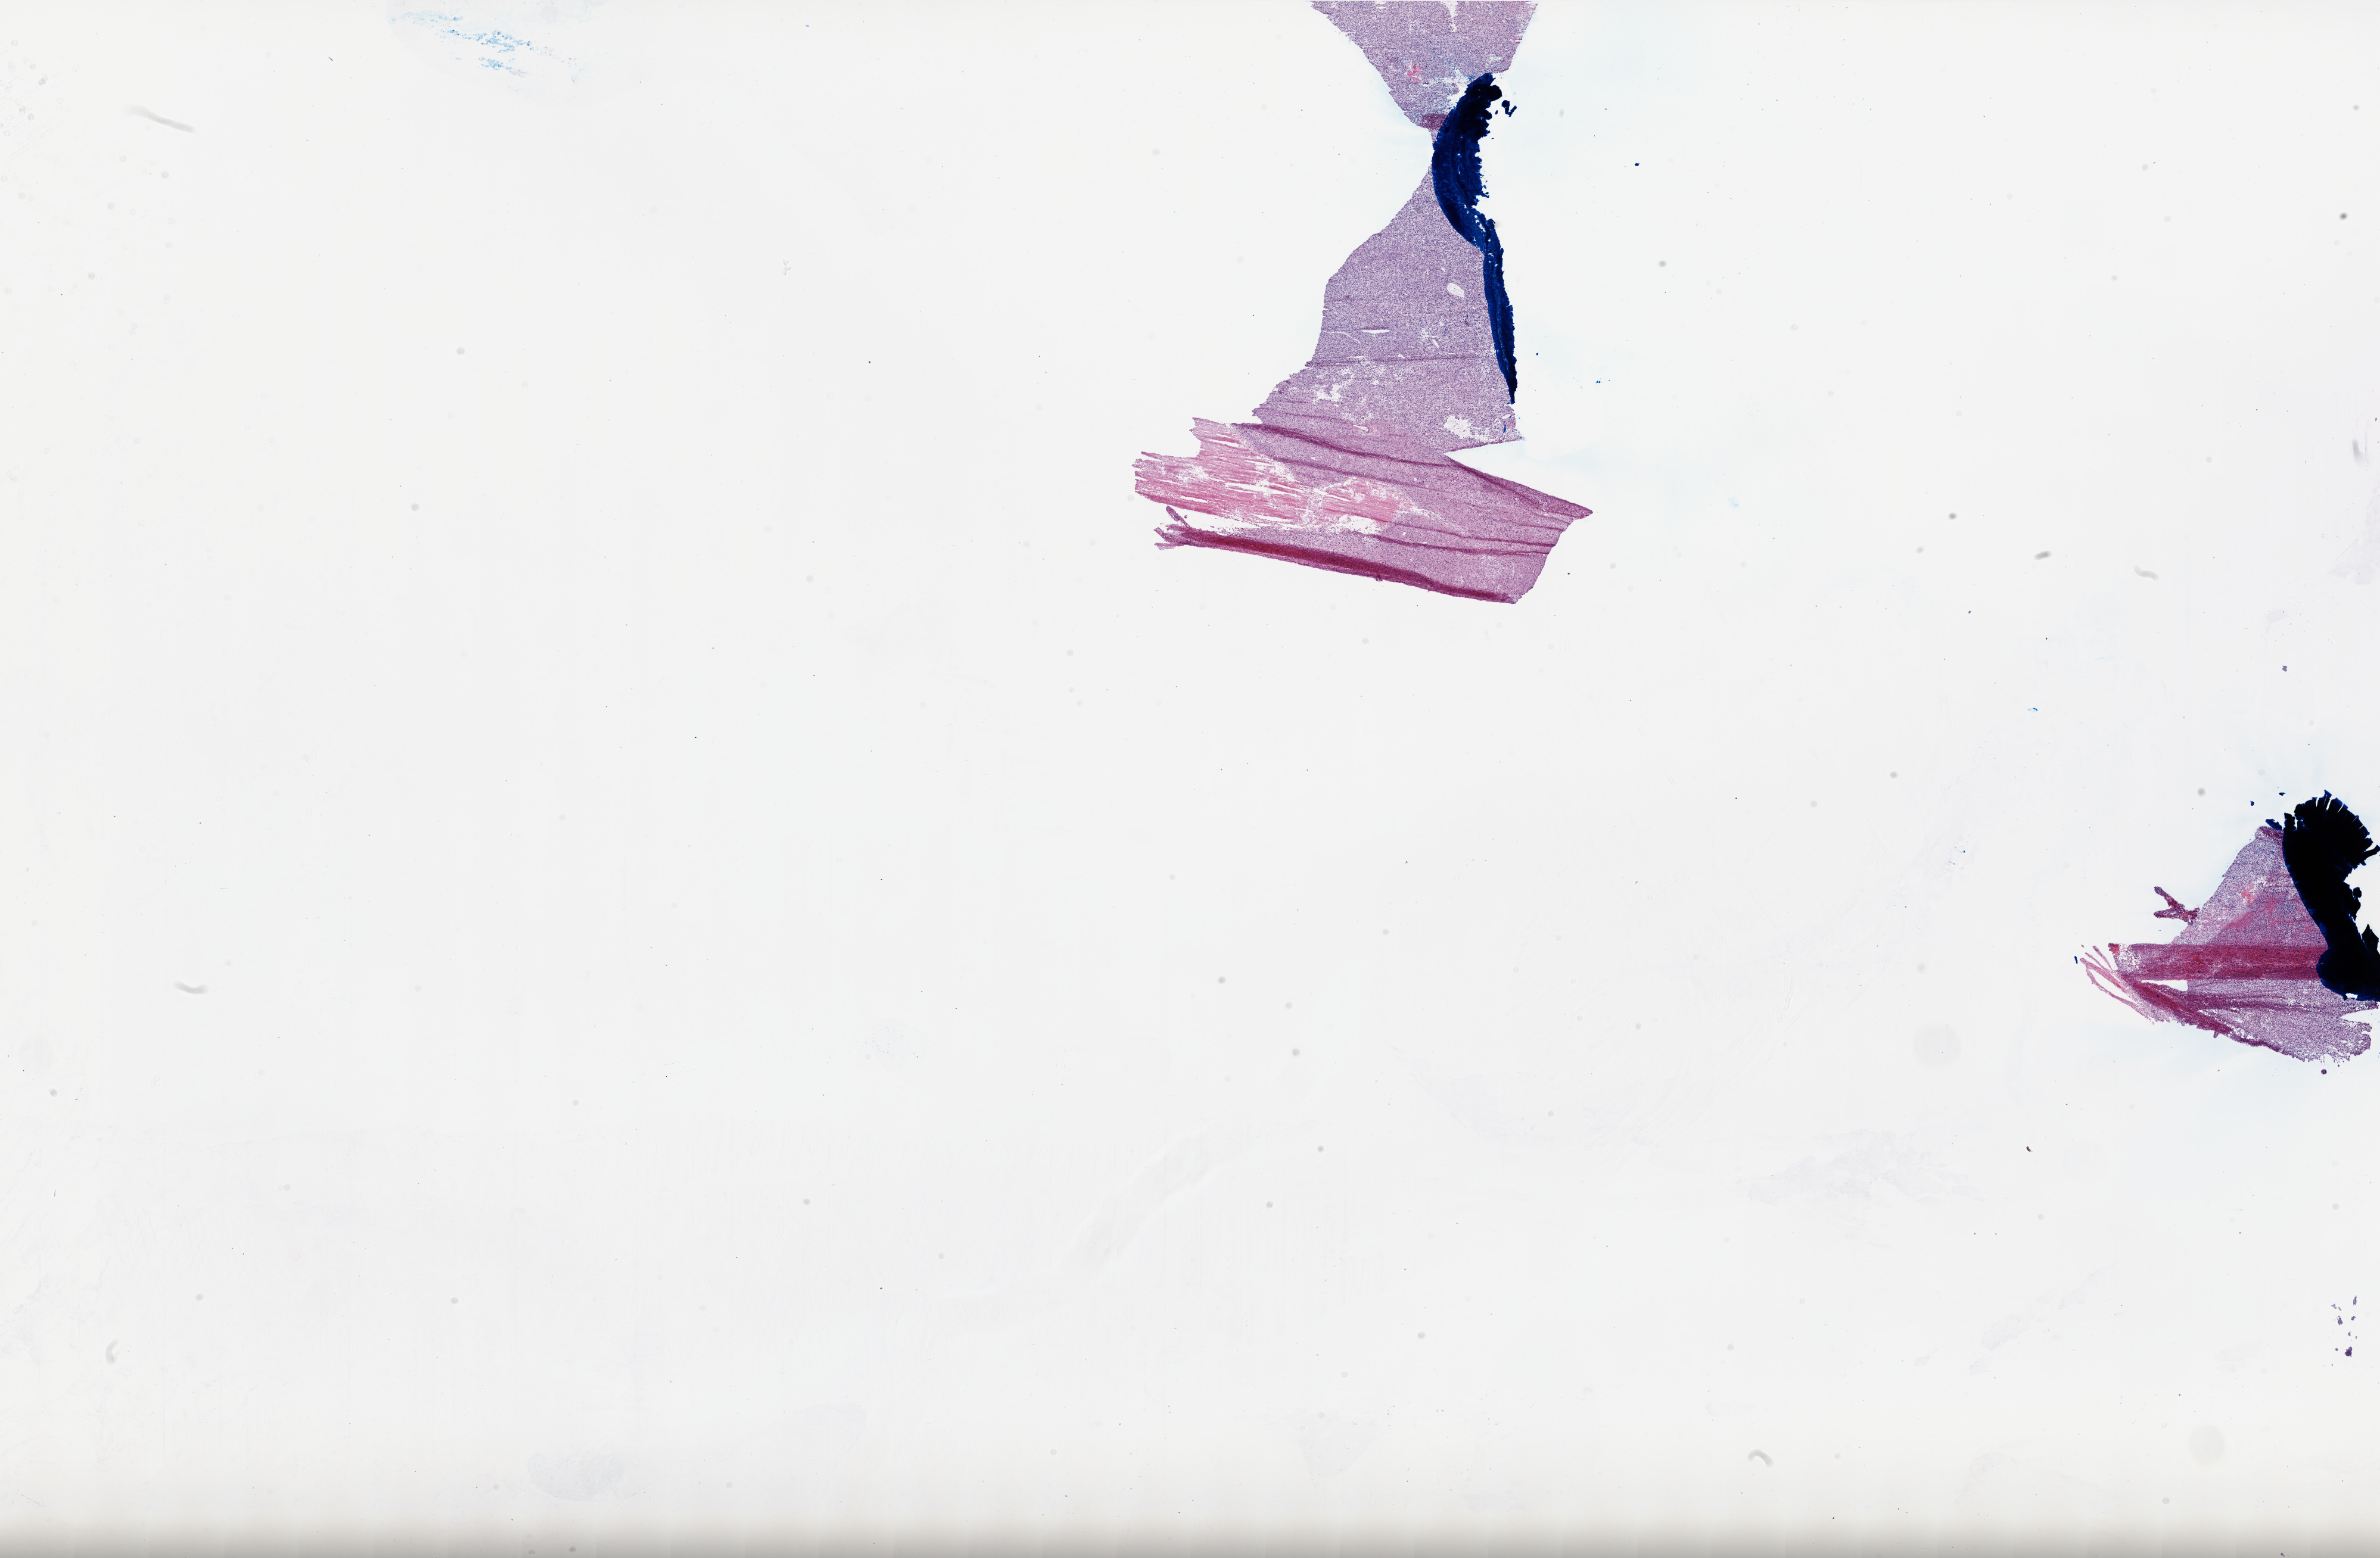
Whole-slide histology image, Hematoxylin and eosin (H&E) stained, a low-resolution overview of the entire scanned area, about 32.0 x 20.9 mm, frozen section from the top of the tissue portion, brain, primary tumour sample. Male, age 71 years at initial diagnosis. Slide review estimates, as recorded: tumour cells 80%, tumour nuclei 90%, normal cells 0%, stromal cells 5%, necrosis 15%.
Diagnosis: Glioblastoma.